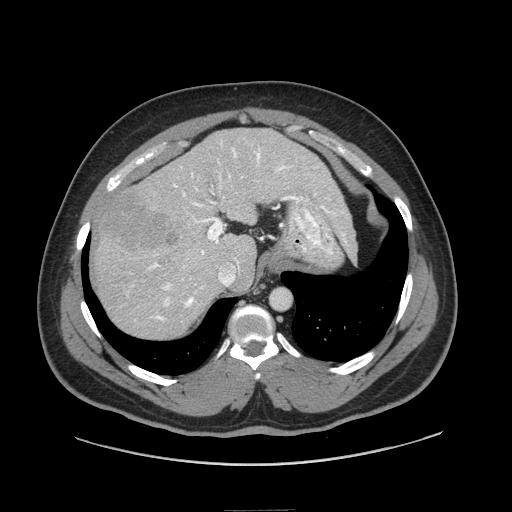
Contrast-enhanced abdominal CT (liver protocol), one axial slice. Position 58 of 87 along the scan axis. Reconstruction kernel STANDARD. 140 kVp. Soft-tissue window (W 400 / L 40 HU). 2.5 mm slice thickness. 512 × 512 image matrix, field of view 440 × 440 mm. From the clinical record (not read from this slice): diagnosis: hepatocellular carcinoma (patient treated with transarterial chemoembolisation; whether this scan precedes or follows treatment is not stated here); TNM stage (as recorded): Stage-II; Child-Pugh class: A; tumour differentiation: moderately differentiated.
Structures marked on this image (semi-automatic segmentation, software-assisted and operator-edited):
- liver parenchyma outside the tumour (the mass and vessels are separate outlines, so this box may not span the whole liver): bounding box <94,128,344,338> (left, top, right, bottom; pixels)
- mass: <97,188,178,251>
- liver vessels: <148,147,323,321>